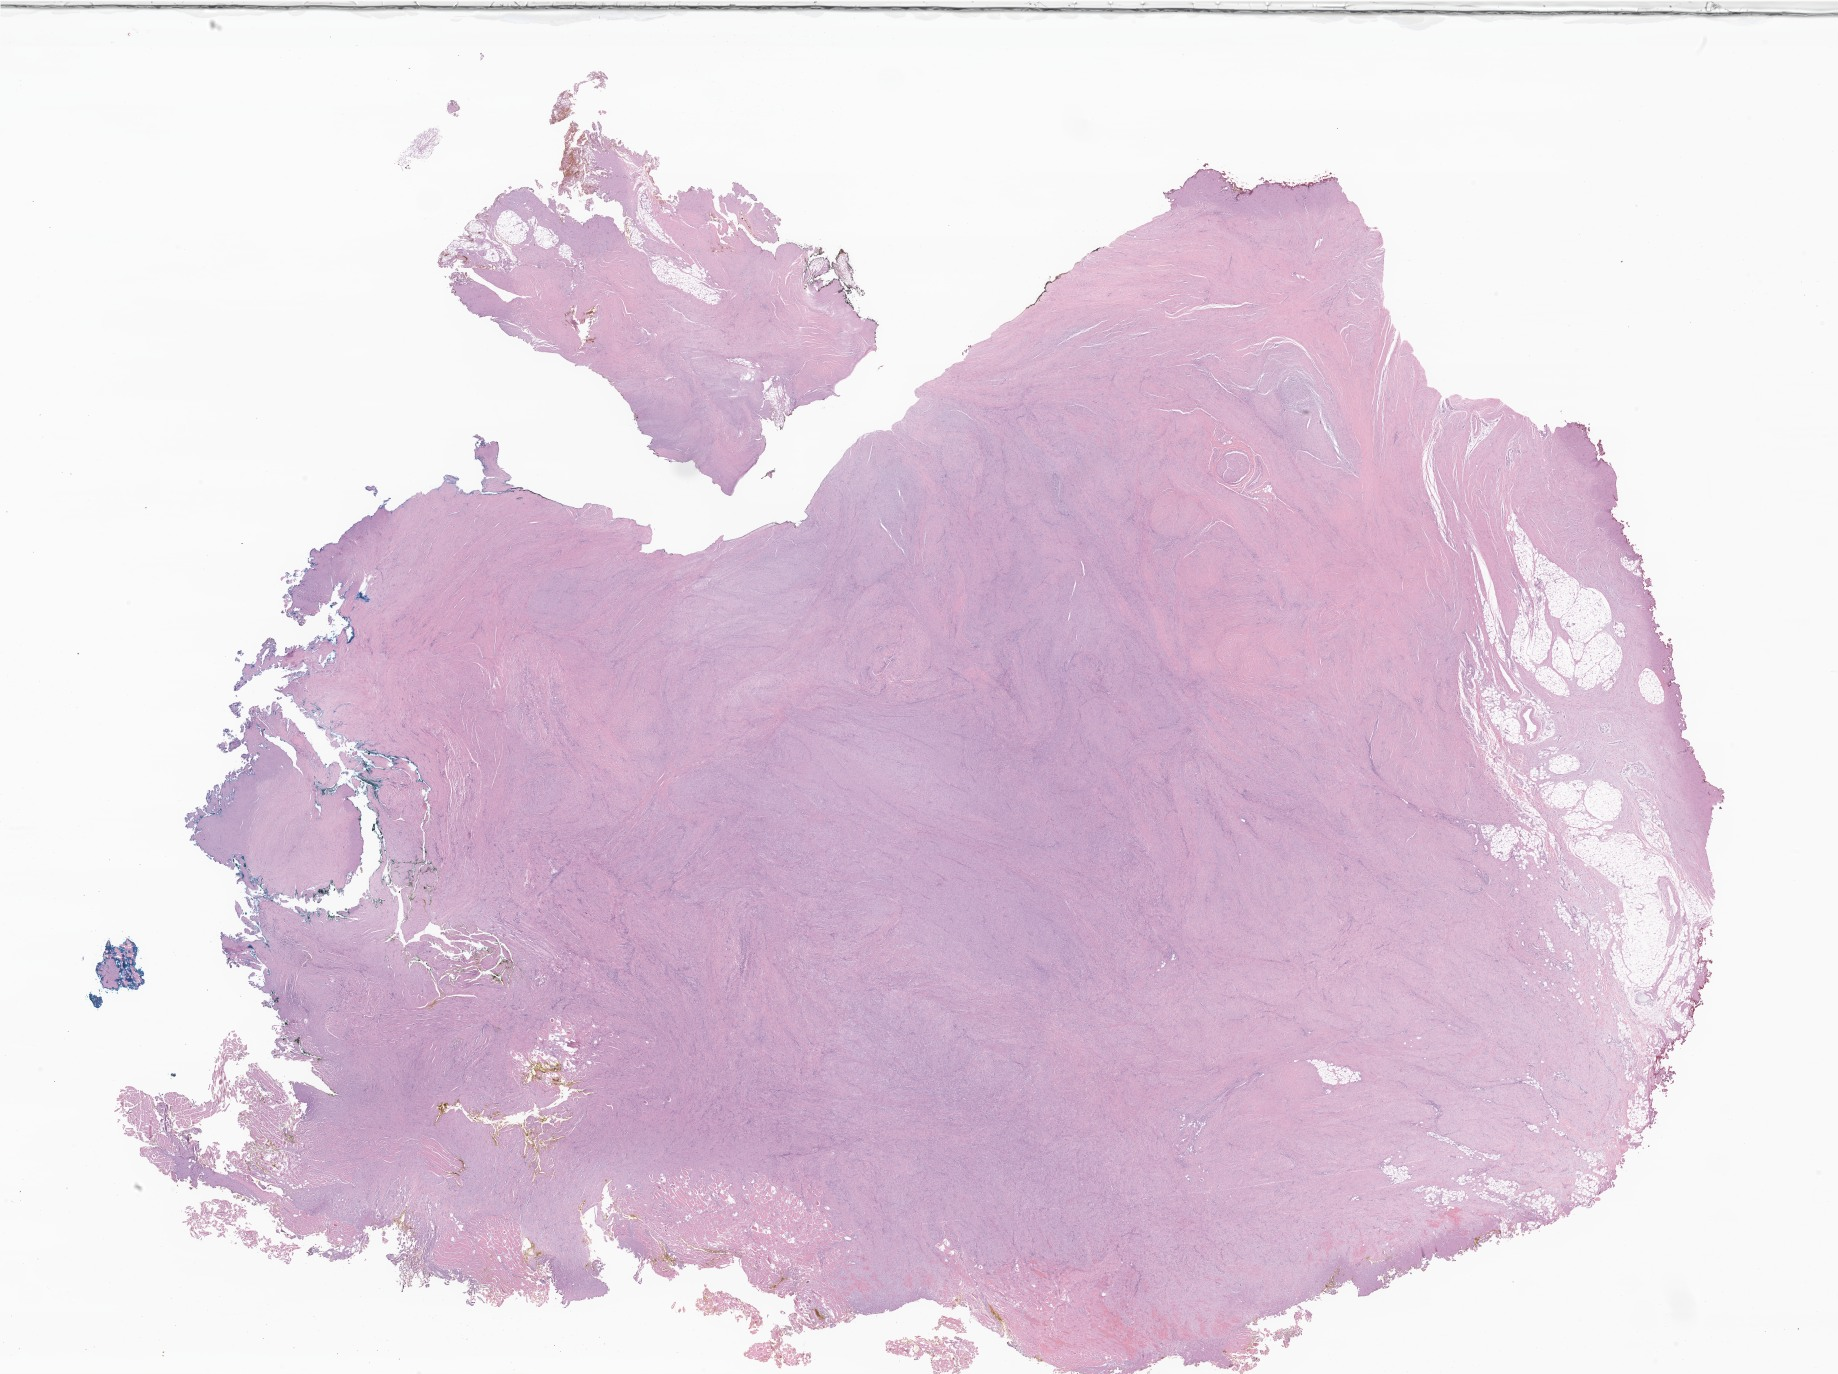
H&E whole-slide image of tumor tissue from the soft tissue of upper extremity, whole scanned area (about 31.0 x 23.2 mm) shown as a low-resolution overview. Formalin-fixed paraffin-embedded section. Patient female; age 67 months.
Diagnosis: Myofibromatosis. Tissue or organ of origin (case record): connective, subcutaneous and other soft tissues of upper limb and shoulder.